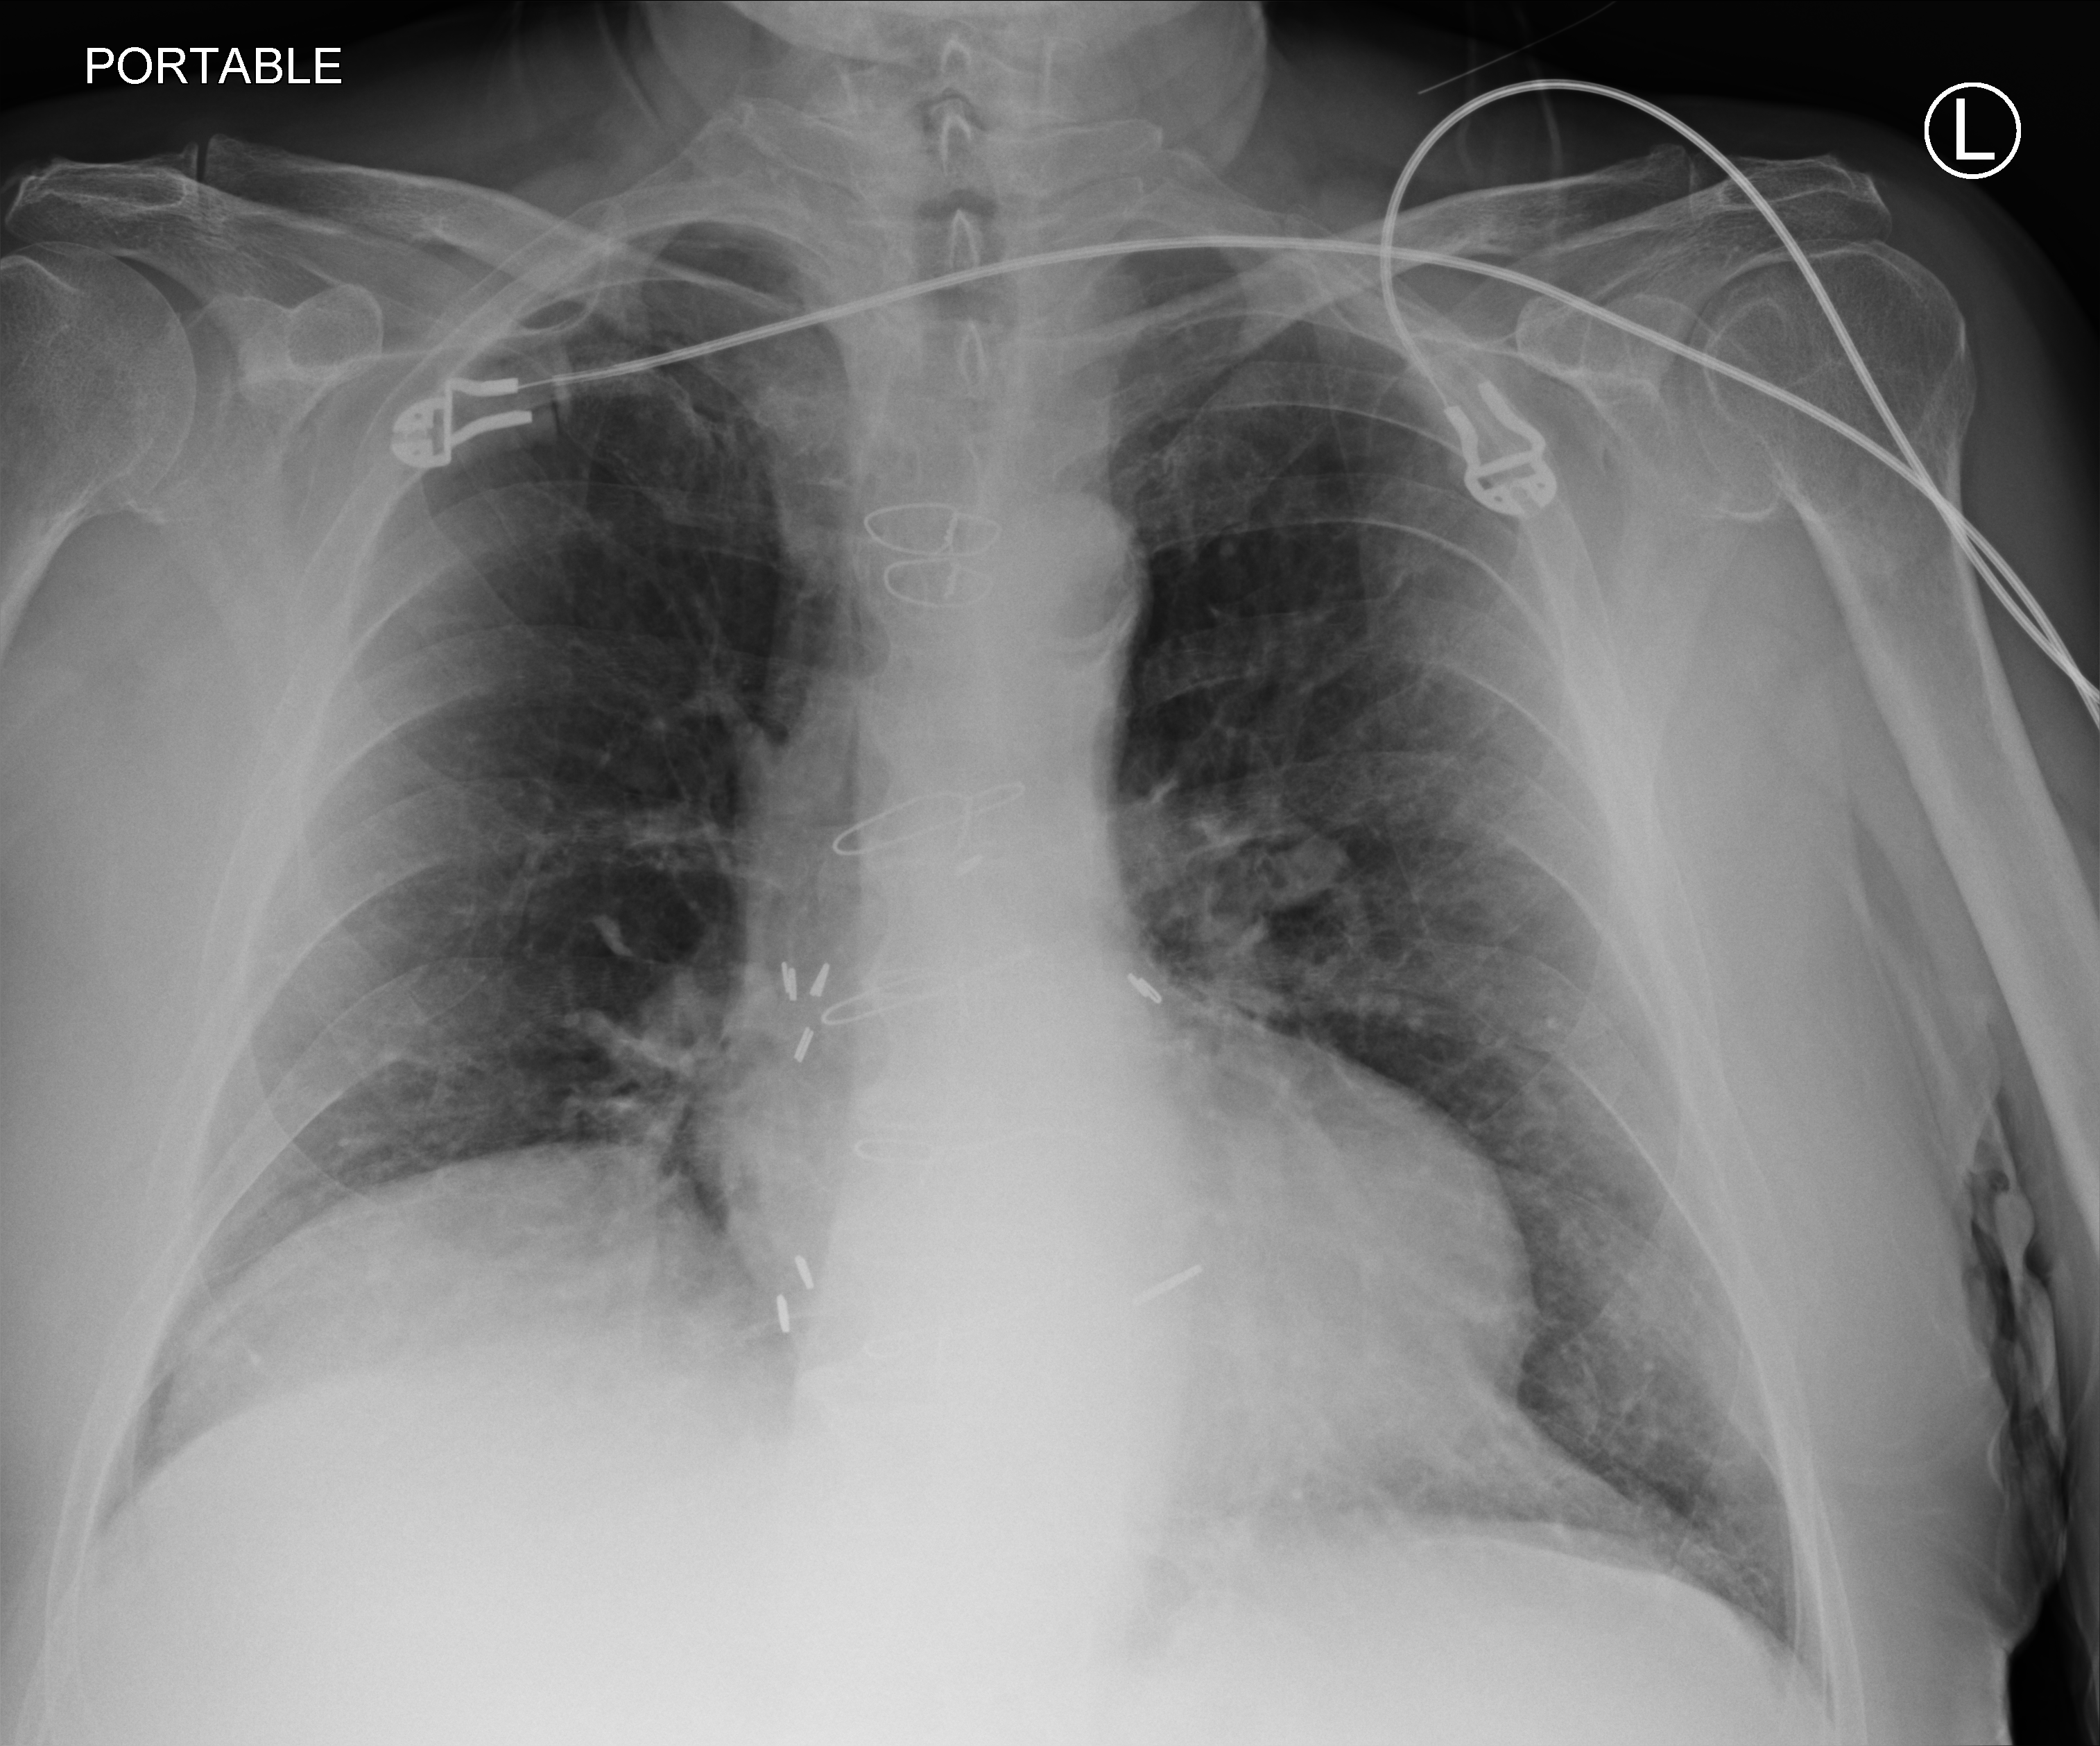
Bedside chest radiograph (computed radiography), anteroposterior (AP) projection. Male patient hospitalised with COVID-19, age 75–90 years.
Admission-level facts for this patient (not findings on this image; timing relative to this image not recorded): diabetes (admission record): yes; COPD (admission record): no.